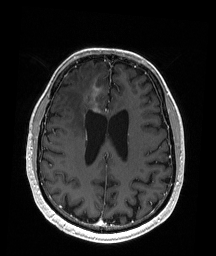
Brain MRI from a brain-tumour surgery series, one axial slice. Slice 73 of 192 in the series (ordered by position). T1-weighted post-contrast. 1 mm slice thickness. 216 × 256 image matrix. Case-level facts recorded for this patient, not image findings: histopathology: Astrocytoma; WHO grade: 3; IDH mutation: yes; tumour location: Right Frontal.
Annotated regions visible in this slice (outlined manually by an expert reader):
- tumour: bounding box (x1, y1, x2, y2) in pixels: (88, 92, 98, 113)